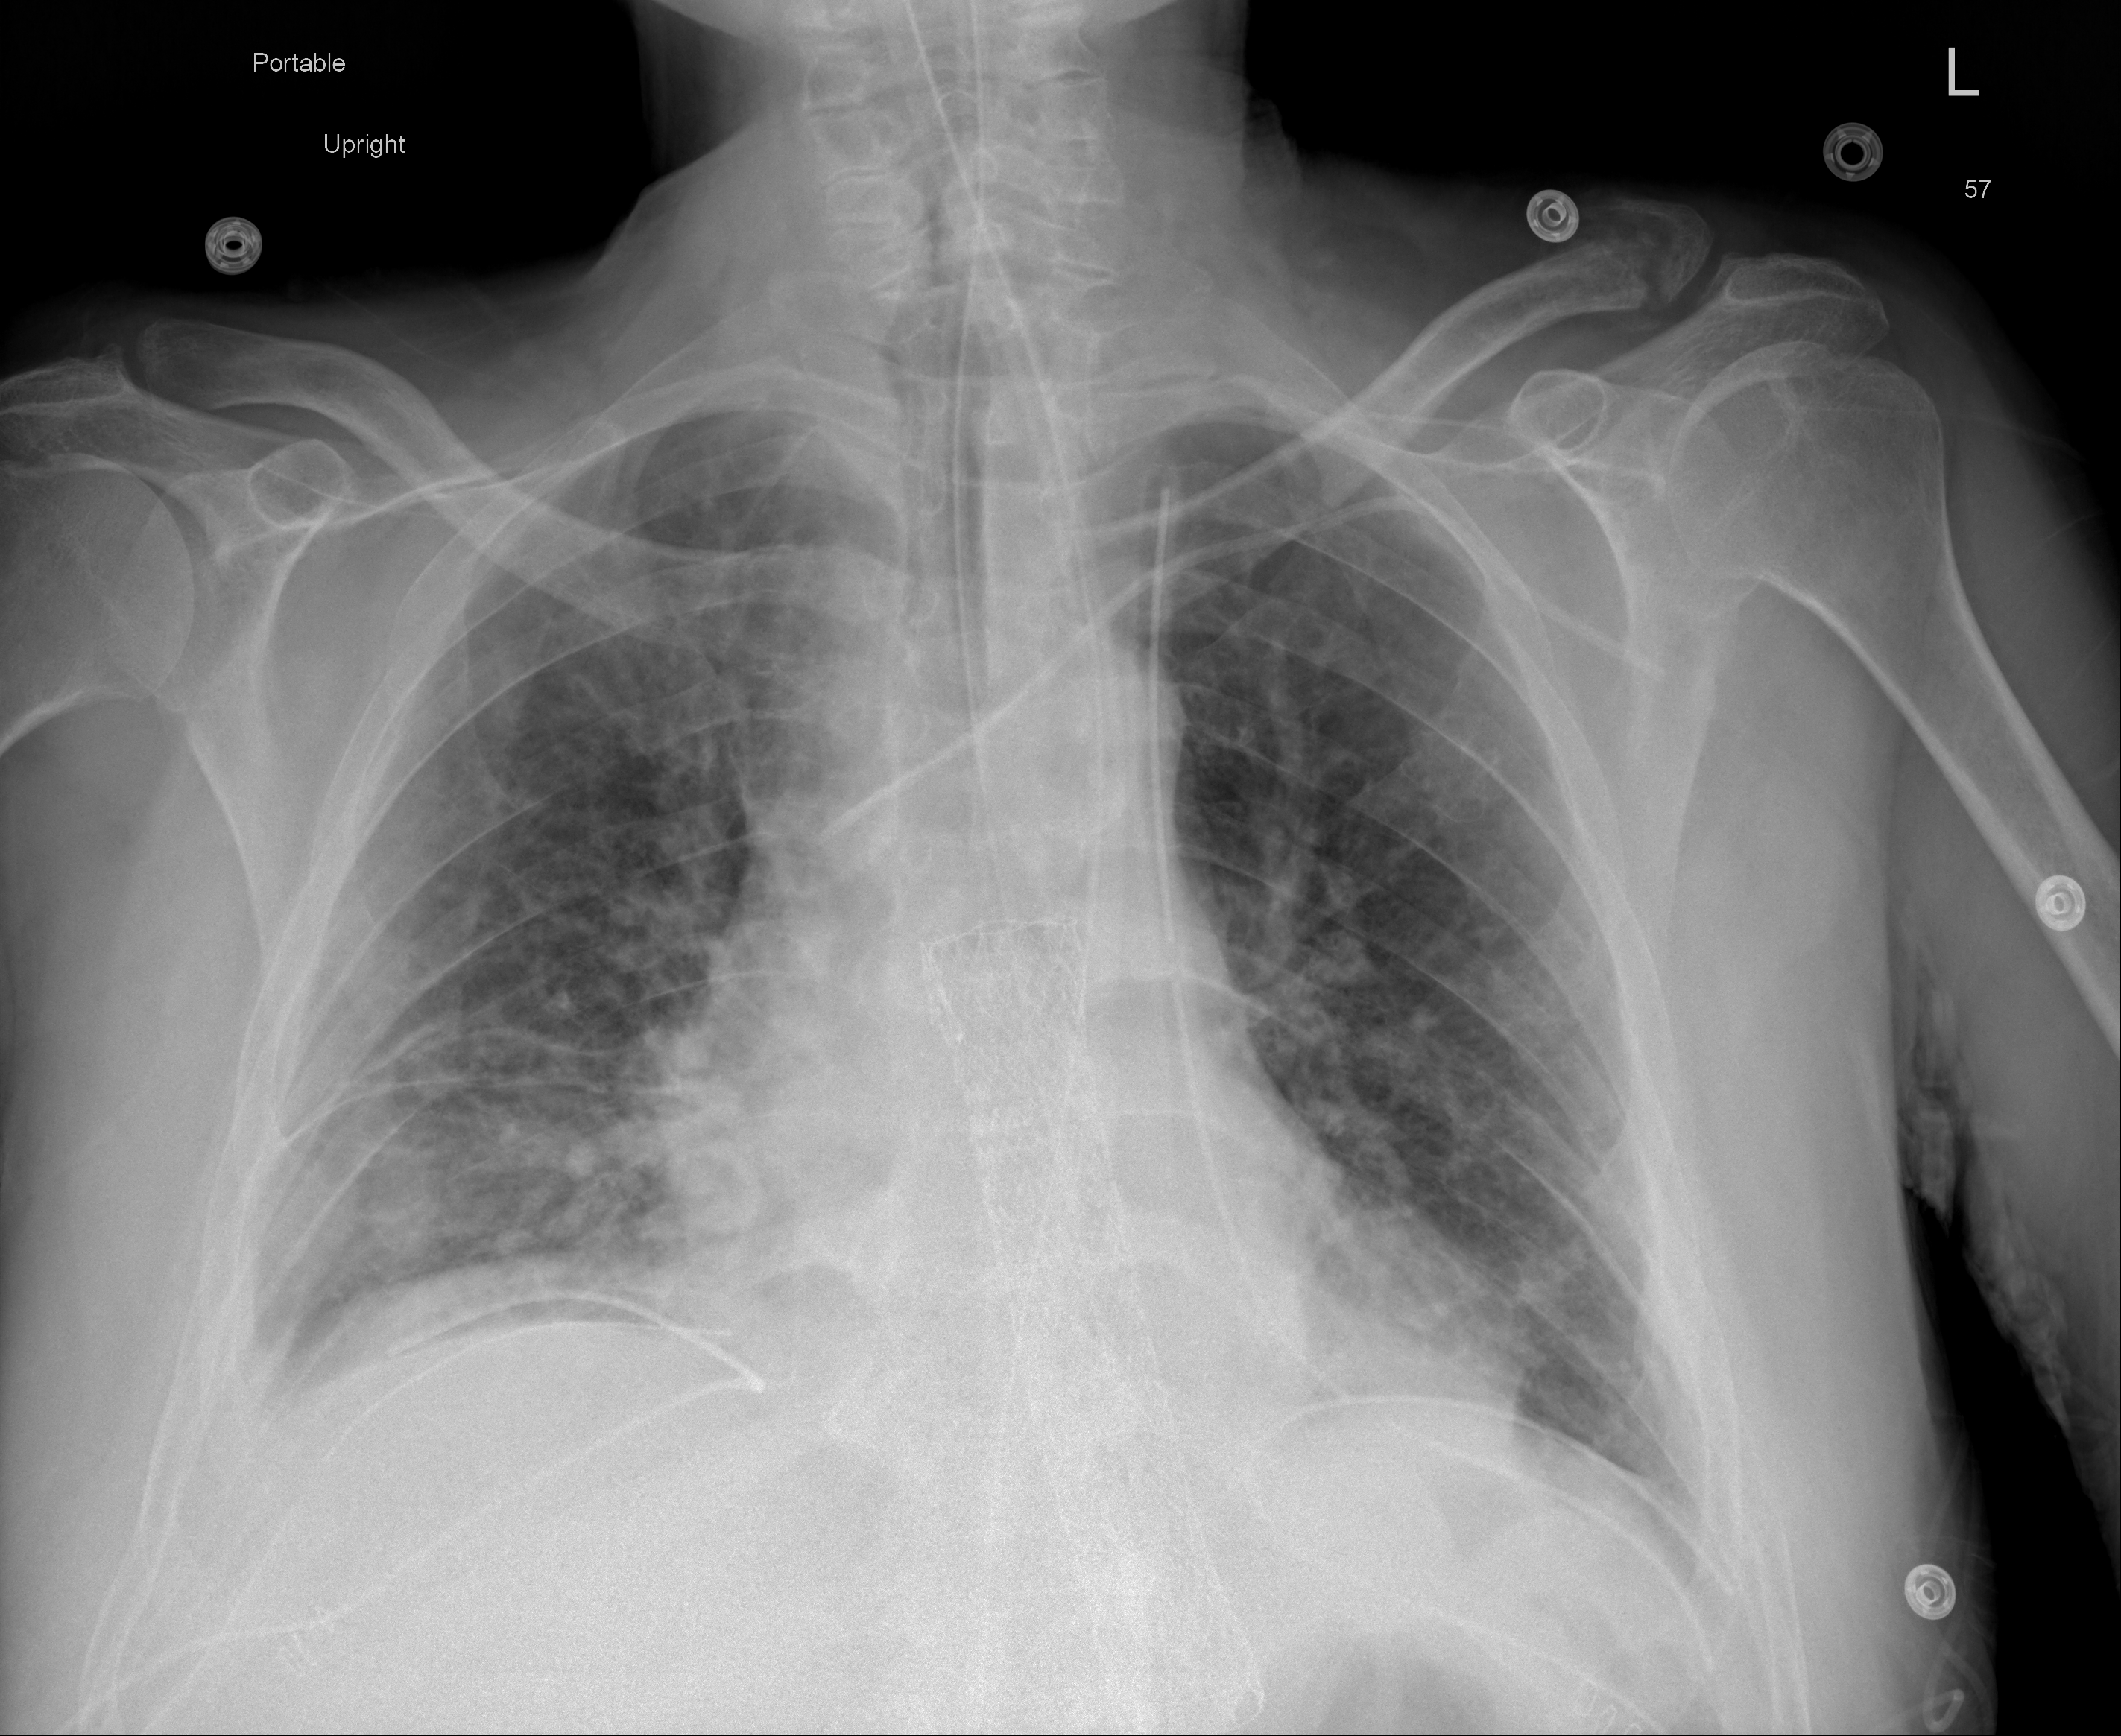
Portable chest radiograph, AP projection. Male patient, age 64 years; imaged 8 days after the COVID-19 diagnosis.
Key findings recorded by the radiologist: Bilateral lower lung atelectatic changes with question of superimposed airspace opacity on both sides, mildly improved.